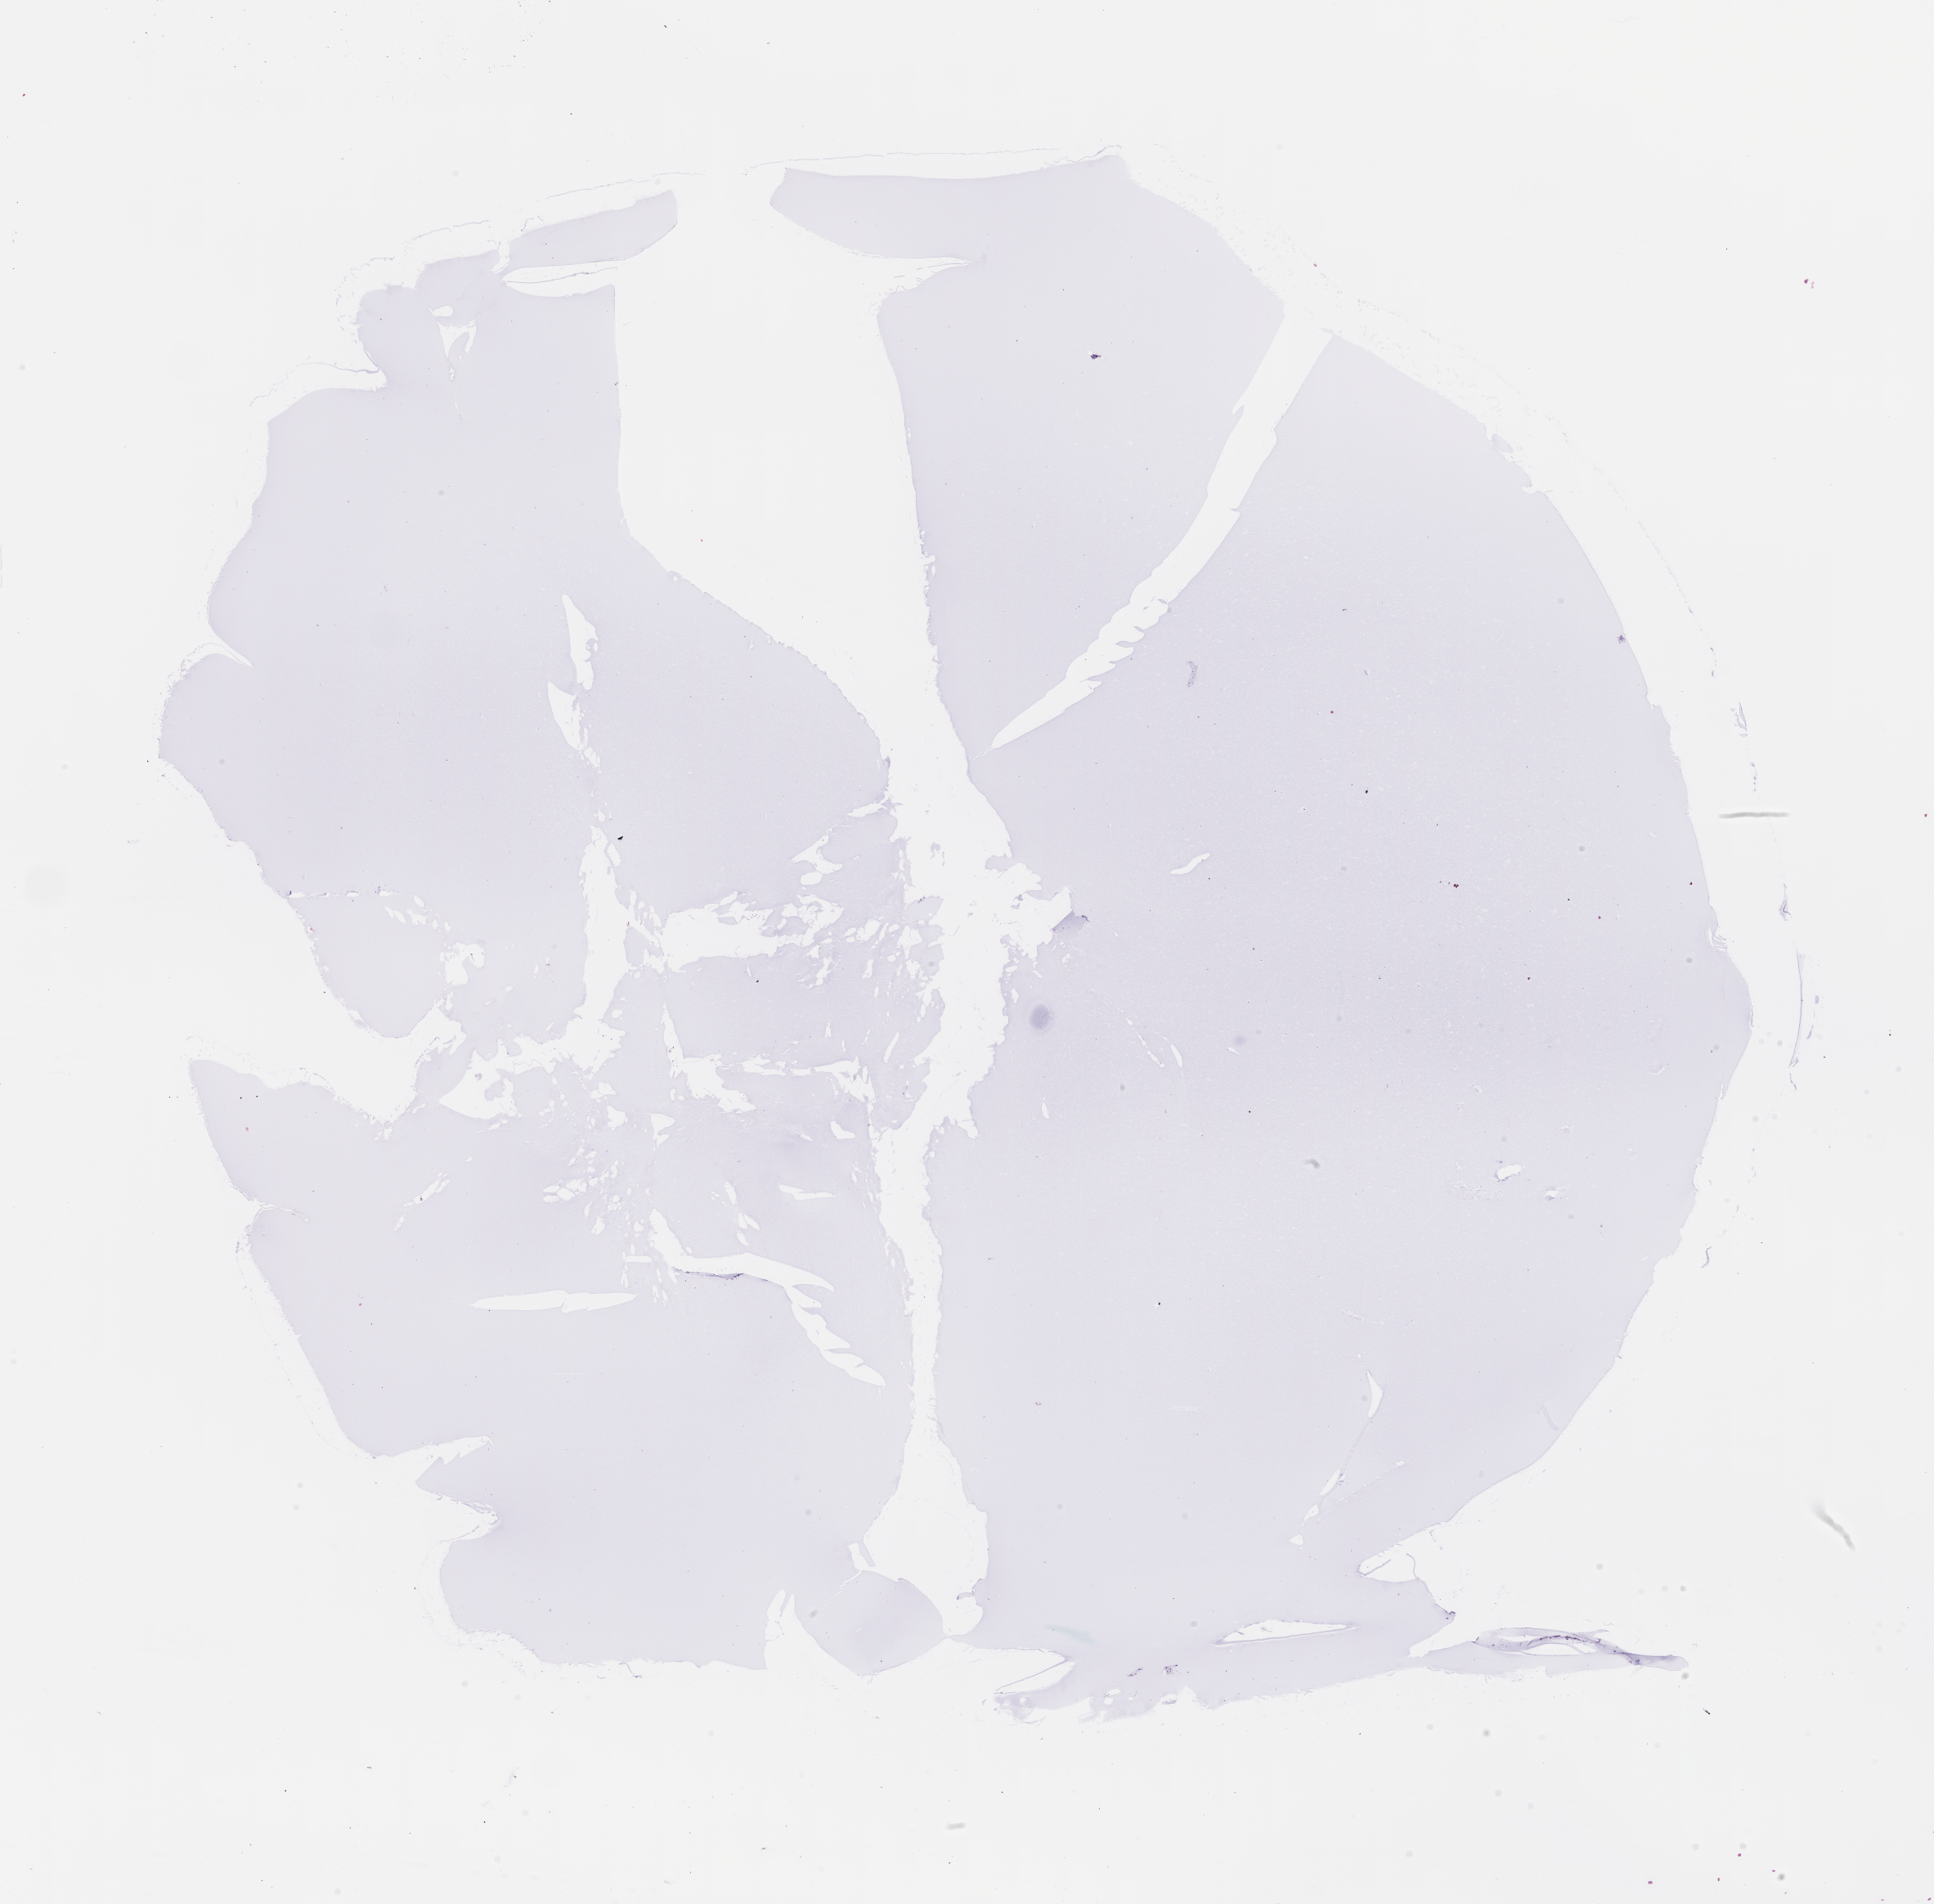
Digitized hematoxylin and eosin (H&E)-stained section — a low-resolution overview of the entire scanned area, about 19.1 x 18.8 mm. Formalin-fixed paraffin-embedded section. Site: lung. Archival tissue. Male patient.
* this section: primary tumor
* diagnosis: Non-Small Cell Lung Carcinoma